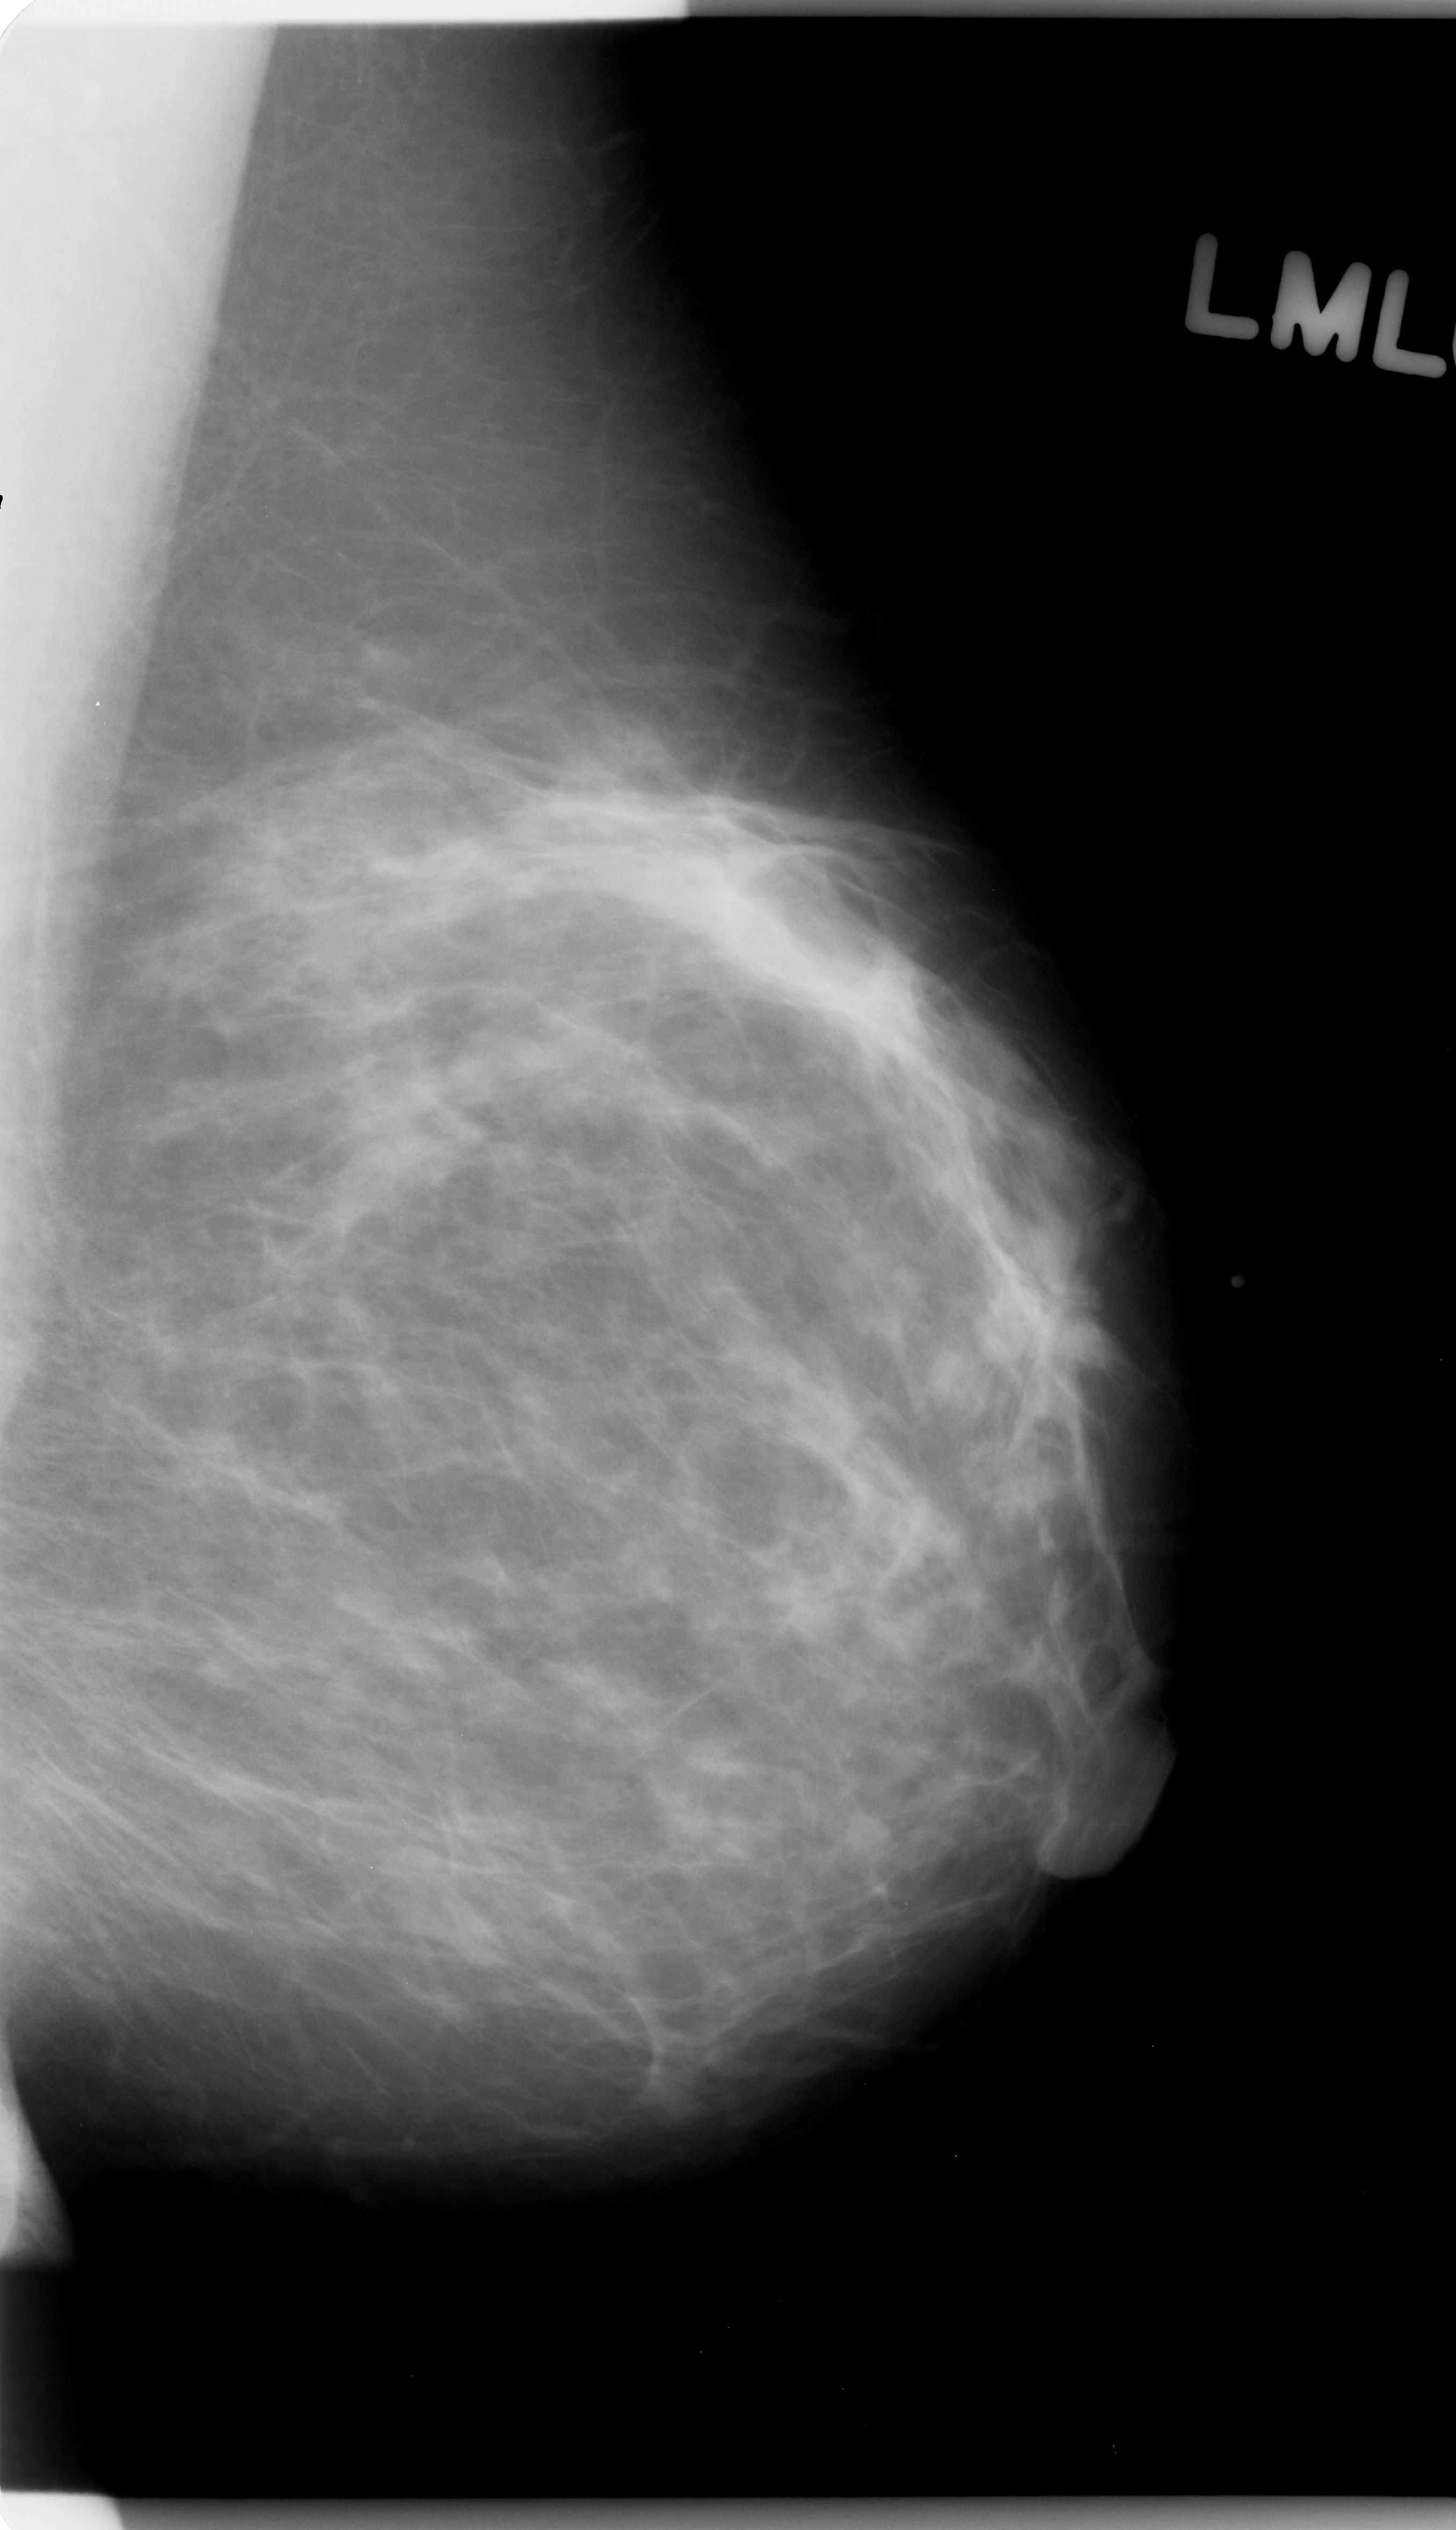
Scanned film-screen mammogram; left breast; mediolateral oblique (MLO) view; breast composition: scattered fibroglandular densities (BI-RADS density category 2 of 4); 1456 × 2530 image matrix.
Marked abnormalities (boxes around the expert regions of interest):
- mass, shape irregular, margins spiculated; BI-RADS assessment category 5; subtlety rating 4 on a 1 (subtle) to 5 (obvious) scale; pathology result (as recorded, not read from the image): malignant: box from (x=911, y=1232) to (x=1110, y=1433) px